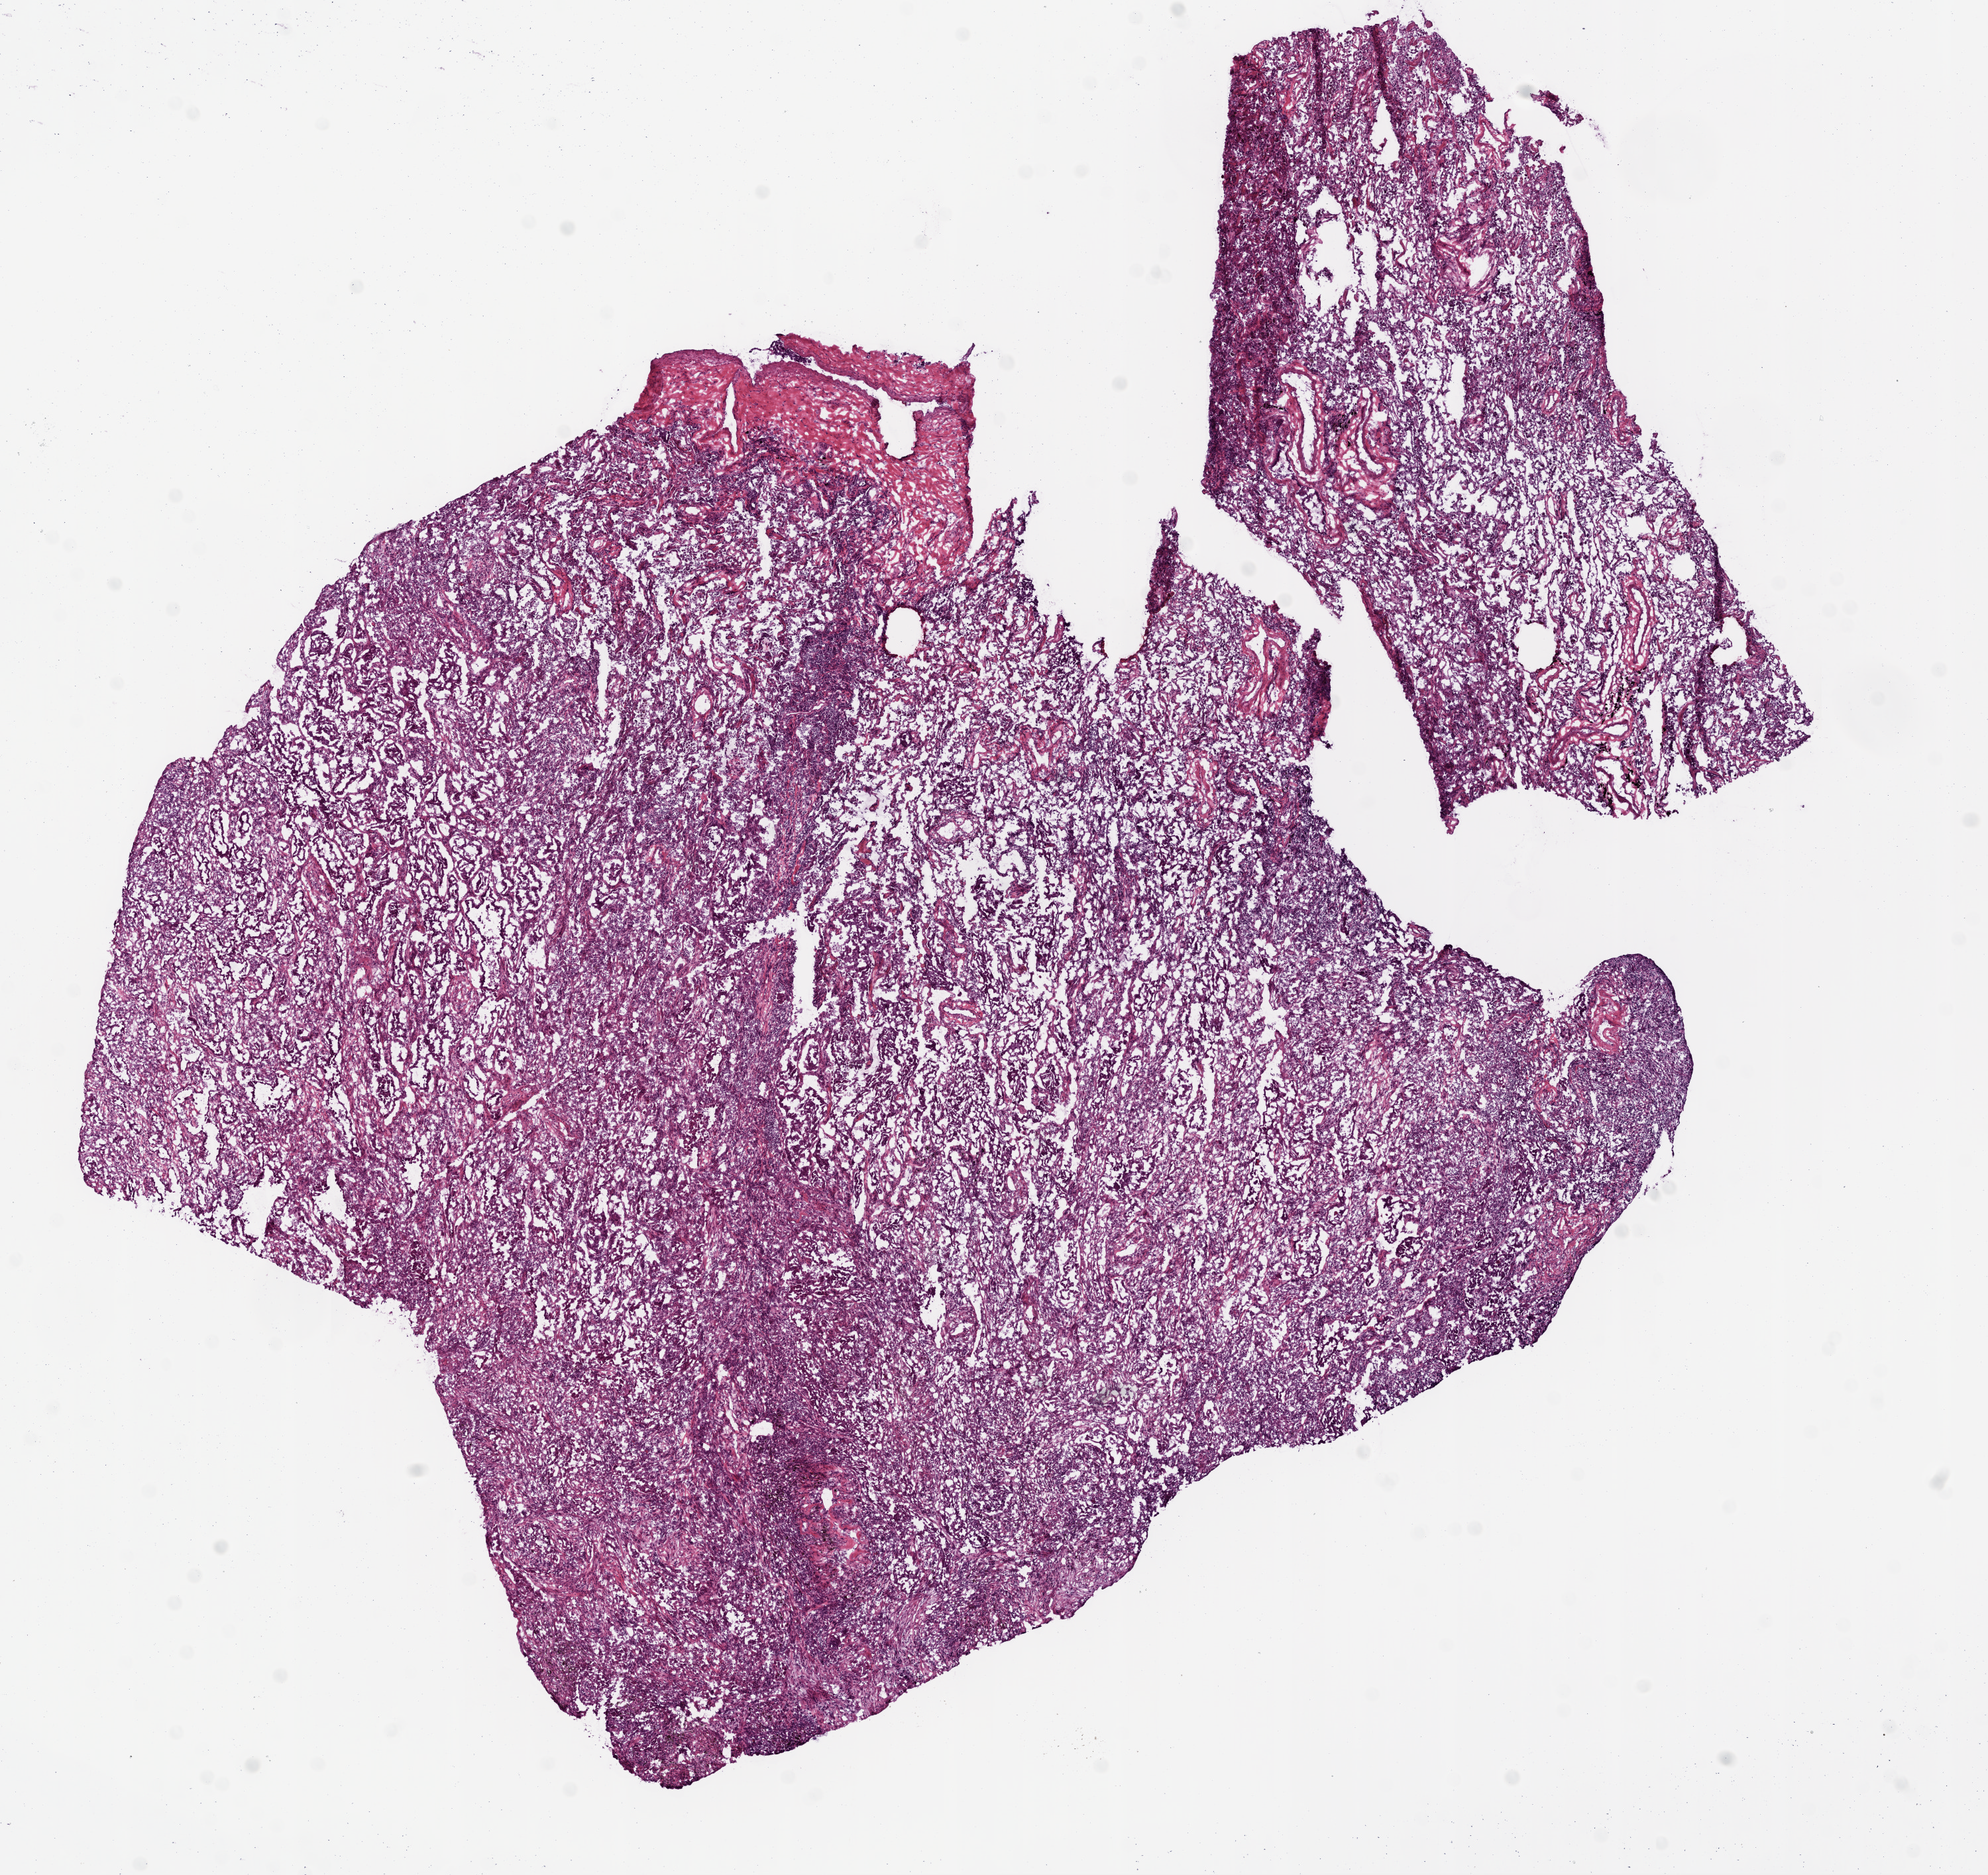
H&E-stained whole-slide image, a low-resolution overview of the entire scanned area, about 12.0 x 11.4 mm. Frozen section from the top of the tissue portion. Lung, primary tumour sample. Female, age 50 years at initial diagnosis. Pathologist review of this section (percent, as recorded): tumour cells 85%, tumour nuclei 60%, normal cells 0%, stromal cells 15%, necrosis 0%.
AJCC pathologic stage: IA. Histologic diagnosis: Adenocarcinoma, NOS (upper lobe, lung).